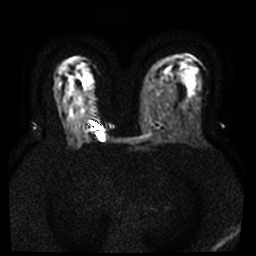
Breast MRI, one axial slice; slice 22 of 40 in the series (ordered by position); diffusion-weighted series; image 2 of 4 stored at this slice position (different b-values; order by instance number); 3 T; 5 mm slice thickness; 256 × 256 image matrix. Female patient.
Annotated regions visible in this slice (manually delineated by an expert):
- tumour on diffusion-weighted imaging: bounding box (x1, y1, x2, y2) in pixels: (98, 134, 104, 140)